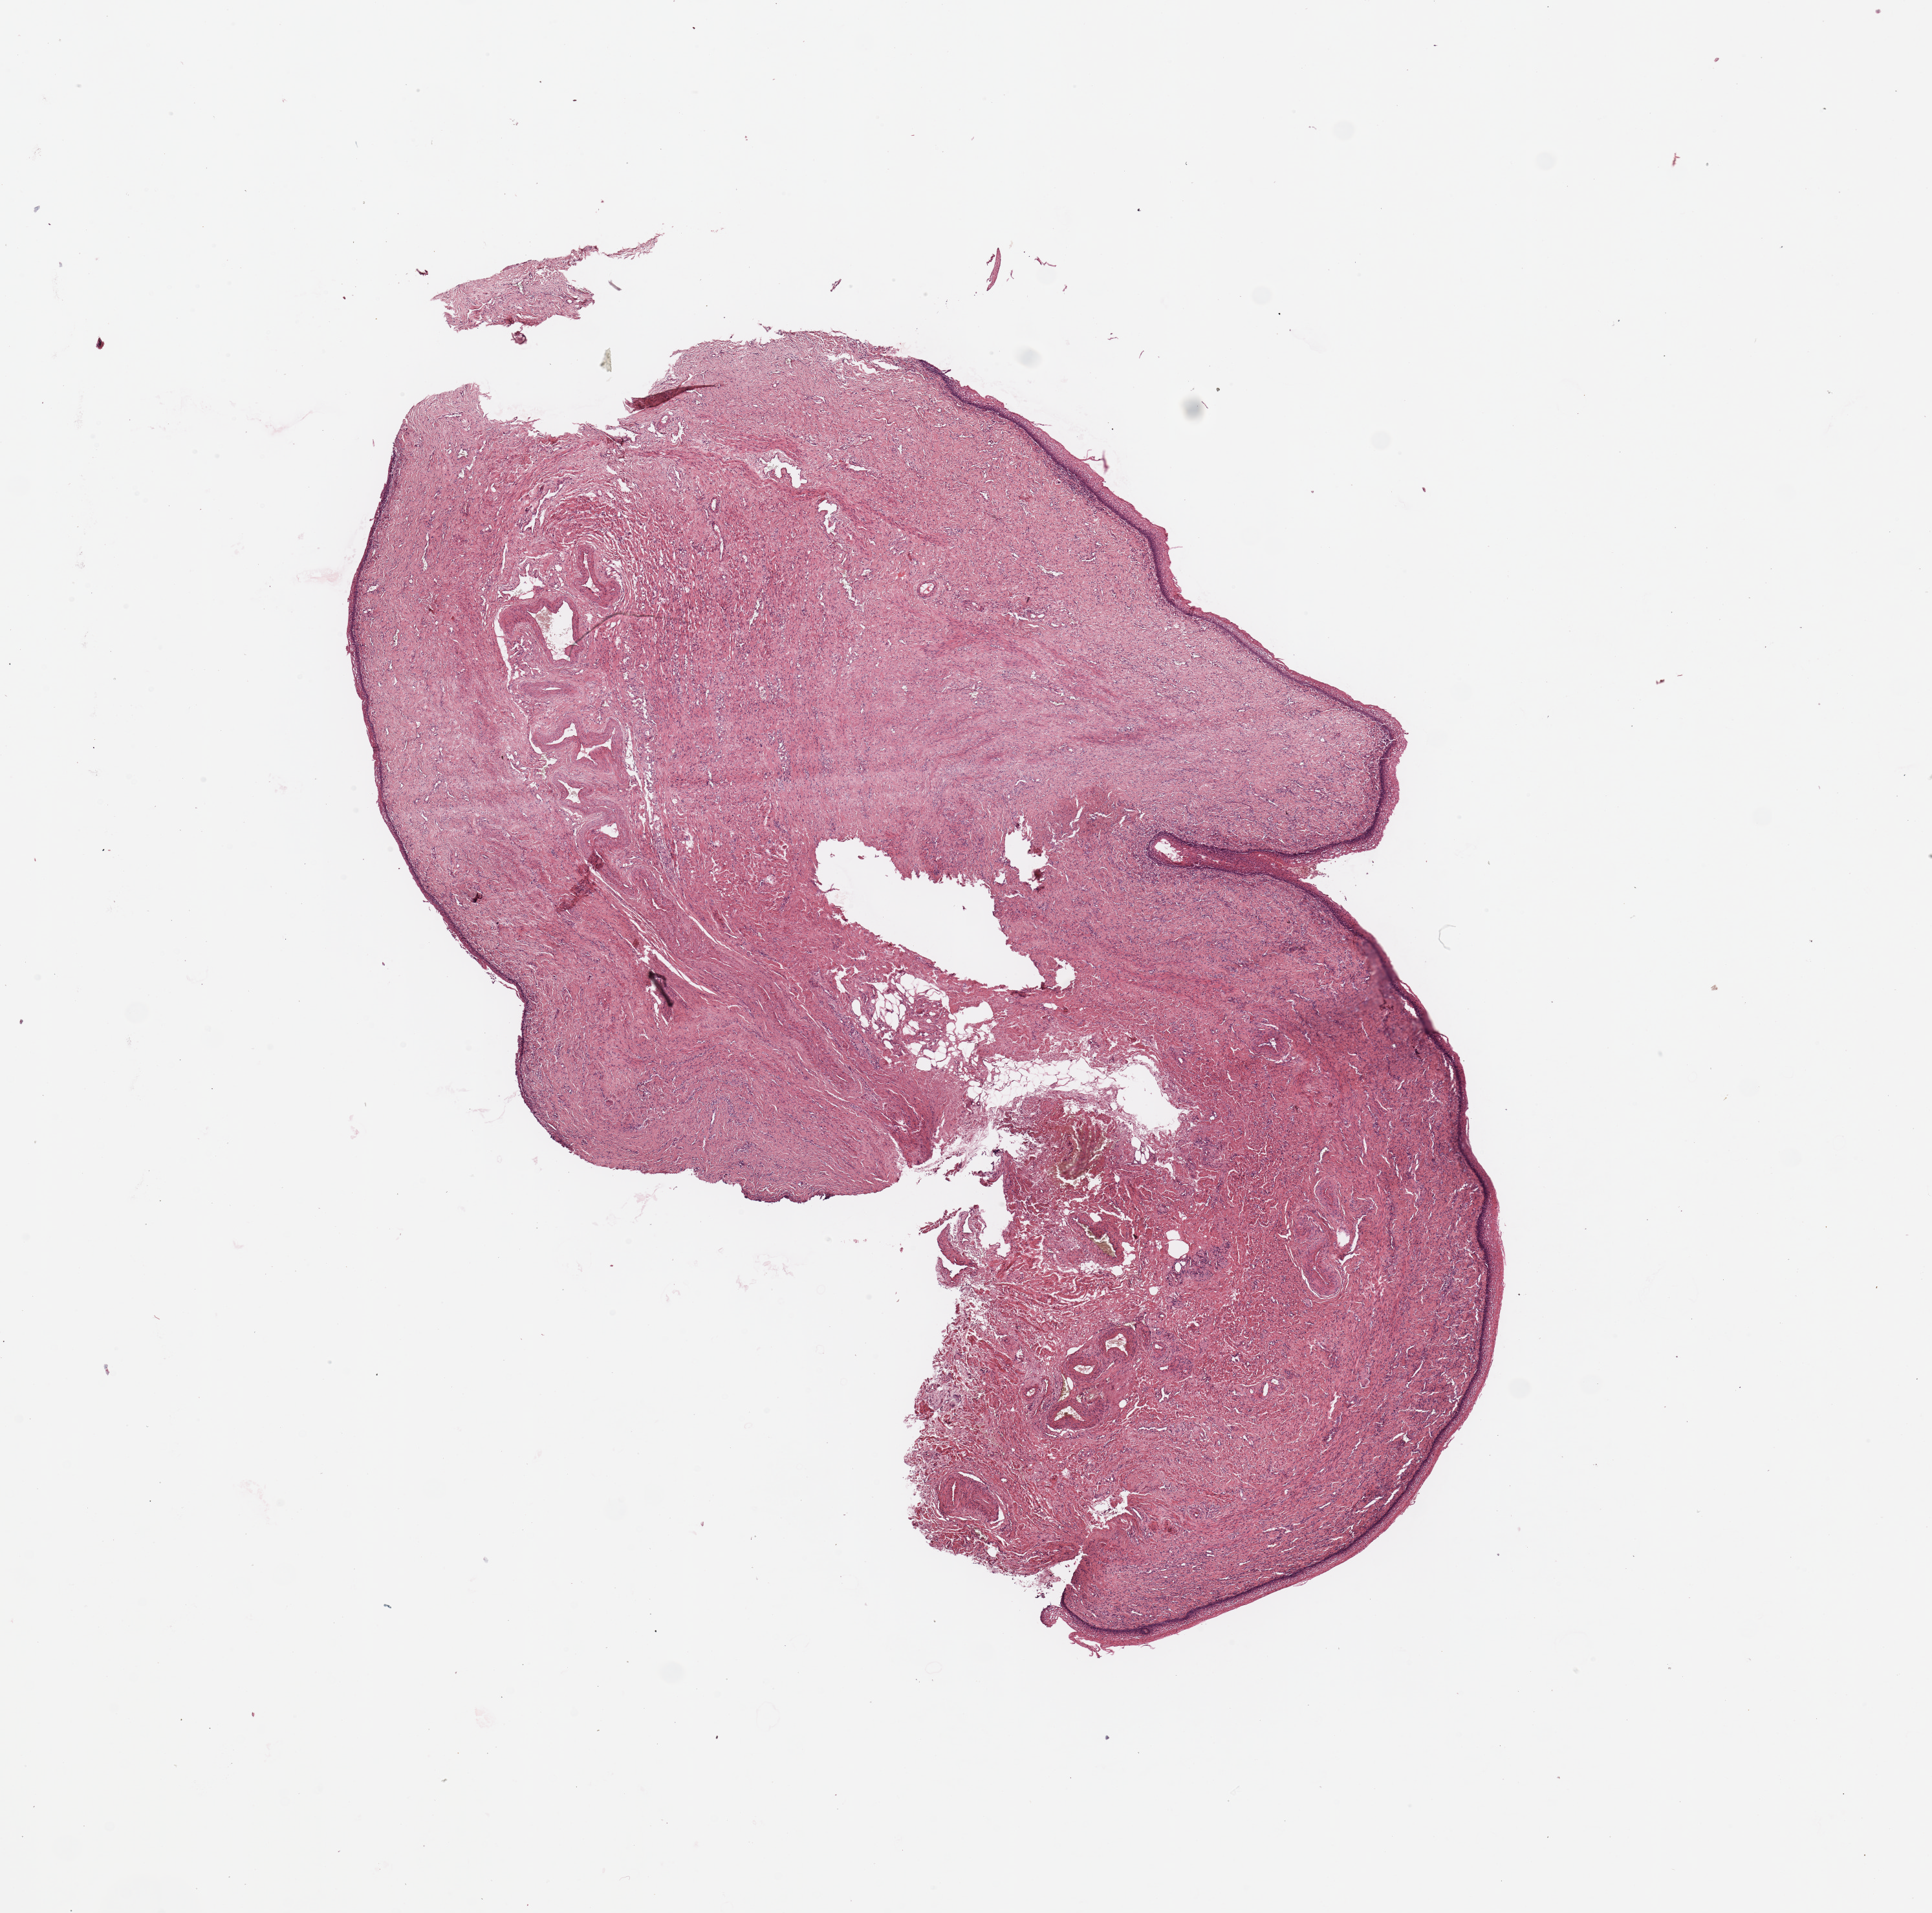
Digitized Hematoxylin and eosin (H&E) stained tissue section (whole slide), a low-resolution overview of the entire scanned area, about 11.8 x 11.7 mm (slide scanned at 20x). Uterus, tissue type not recorded.
Patient diagnosis (cohort enrolment): corpus endometrial carcinoma (uterus).